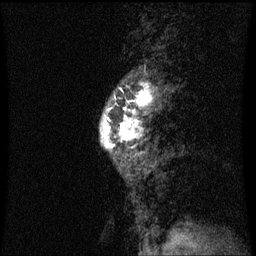
Breast MRI (dynamic contrast-enhanced), one sagittal slice. Slice 20 of 60 in the series (ordered by position). Dynamic contrast-enhanced series, image 2 of 3 at this slice position (ordered by acquisition). 1.5 T. TE 4.2 ms, TR 8.9 ms. 256 × 256 image matrix, field of view 200 × 200 mm. Female patient, age 50 years. From the clinical record (not read from this slice): setting: breast cancer imaged before/during neoadjuvant chemotherapy; receptor status: triple-negative.
Outlined on this slice (semi-automatic segmentation, software-assisted and operator-edited):
- analysis volume of interest (the breast-tissue region the enhancement analysis was run in; not a lesion): bounding box [x1, y1, x2, y2] px = [100, 84, 165, 169]
- tumour enhancement mask (voxels above the 70 % enhancement threshold inside the analysis volume of interest): [106, 84, 153, 149]